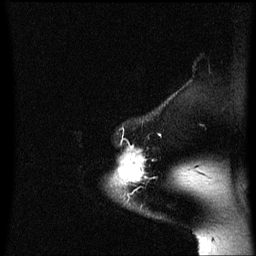
Breast MRI (dynamic contrast-enhanced), one sagittal slice. Position 54 of 60 along the scan axis. Dynamic contrast-enhanced series, image 2 of 3 at this slice position (ordered by acquisition). 1.5 T. TE 4.2 ms, TR 8.4 ms. 2 mm slice thickness. 256 × 256 image matrix, field of view 200 × 200 mm. Patient: female, 54 years. From the clinical record (not read from this slice): setting: breast cancer imaged before/during neoadjuvant chemotherapy; receptor status: HR-positive, HER2-negative.
Structures marked on this image (semi-automatic segmentation, software-assisted and operator-edited):
- analysis volume of interest (the breast-tissue region the enhancement analysis was run in; not a lesion): bounding box [x1, y1, x2, y2] px = [116, 146, 149, 199]
- tumour enhancement mask (voxels above the 70 % enhancement threshold inside the analysis volume of interest): [116, 150, 146, 187]